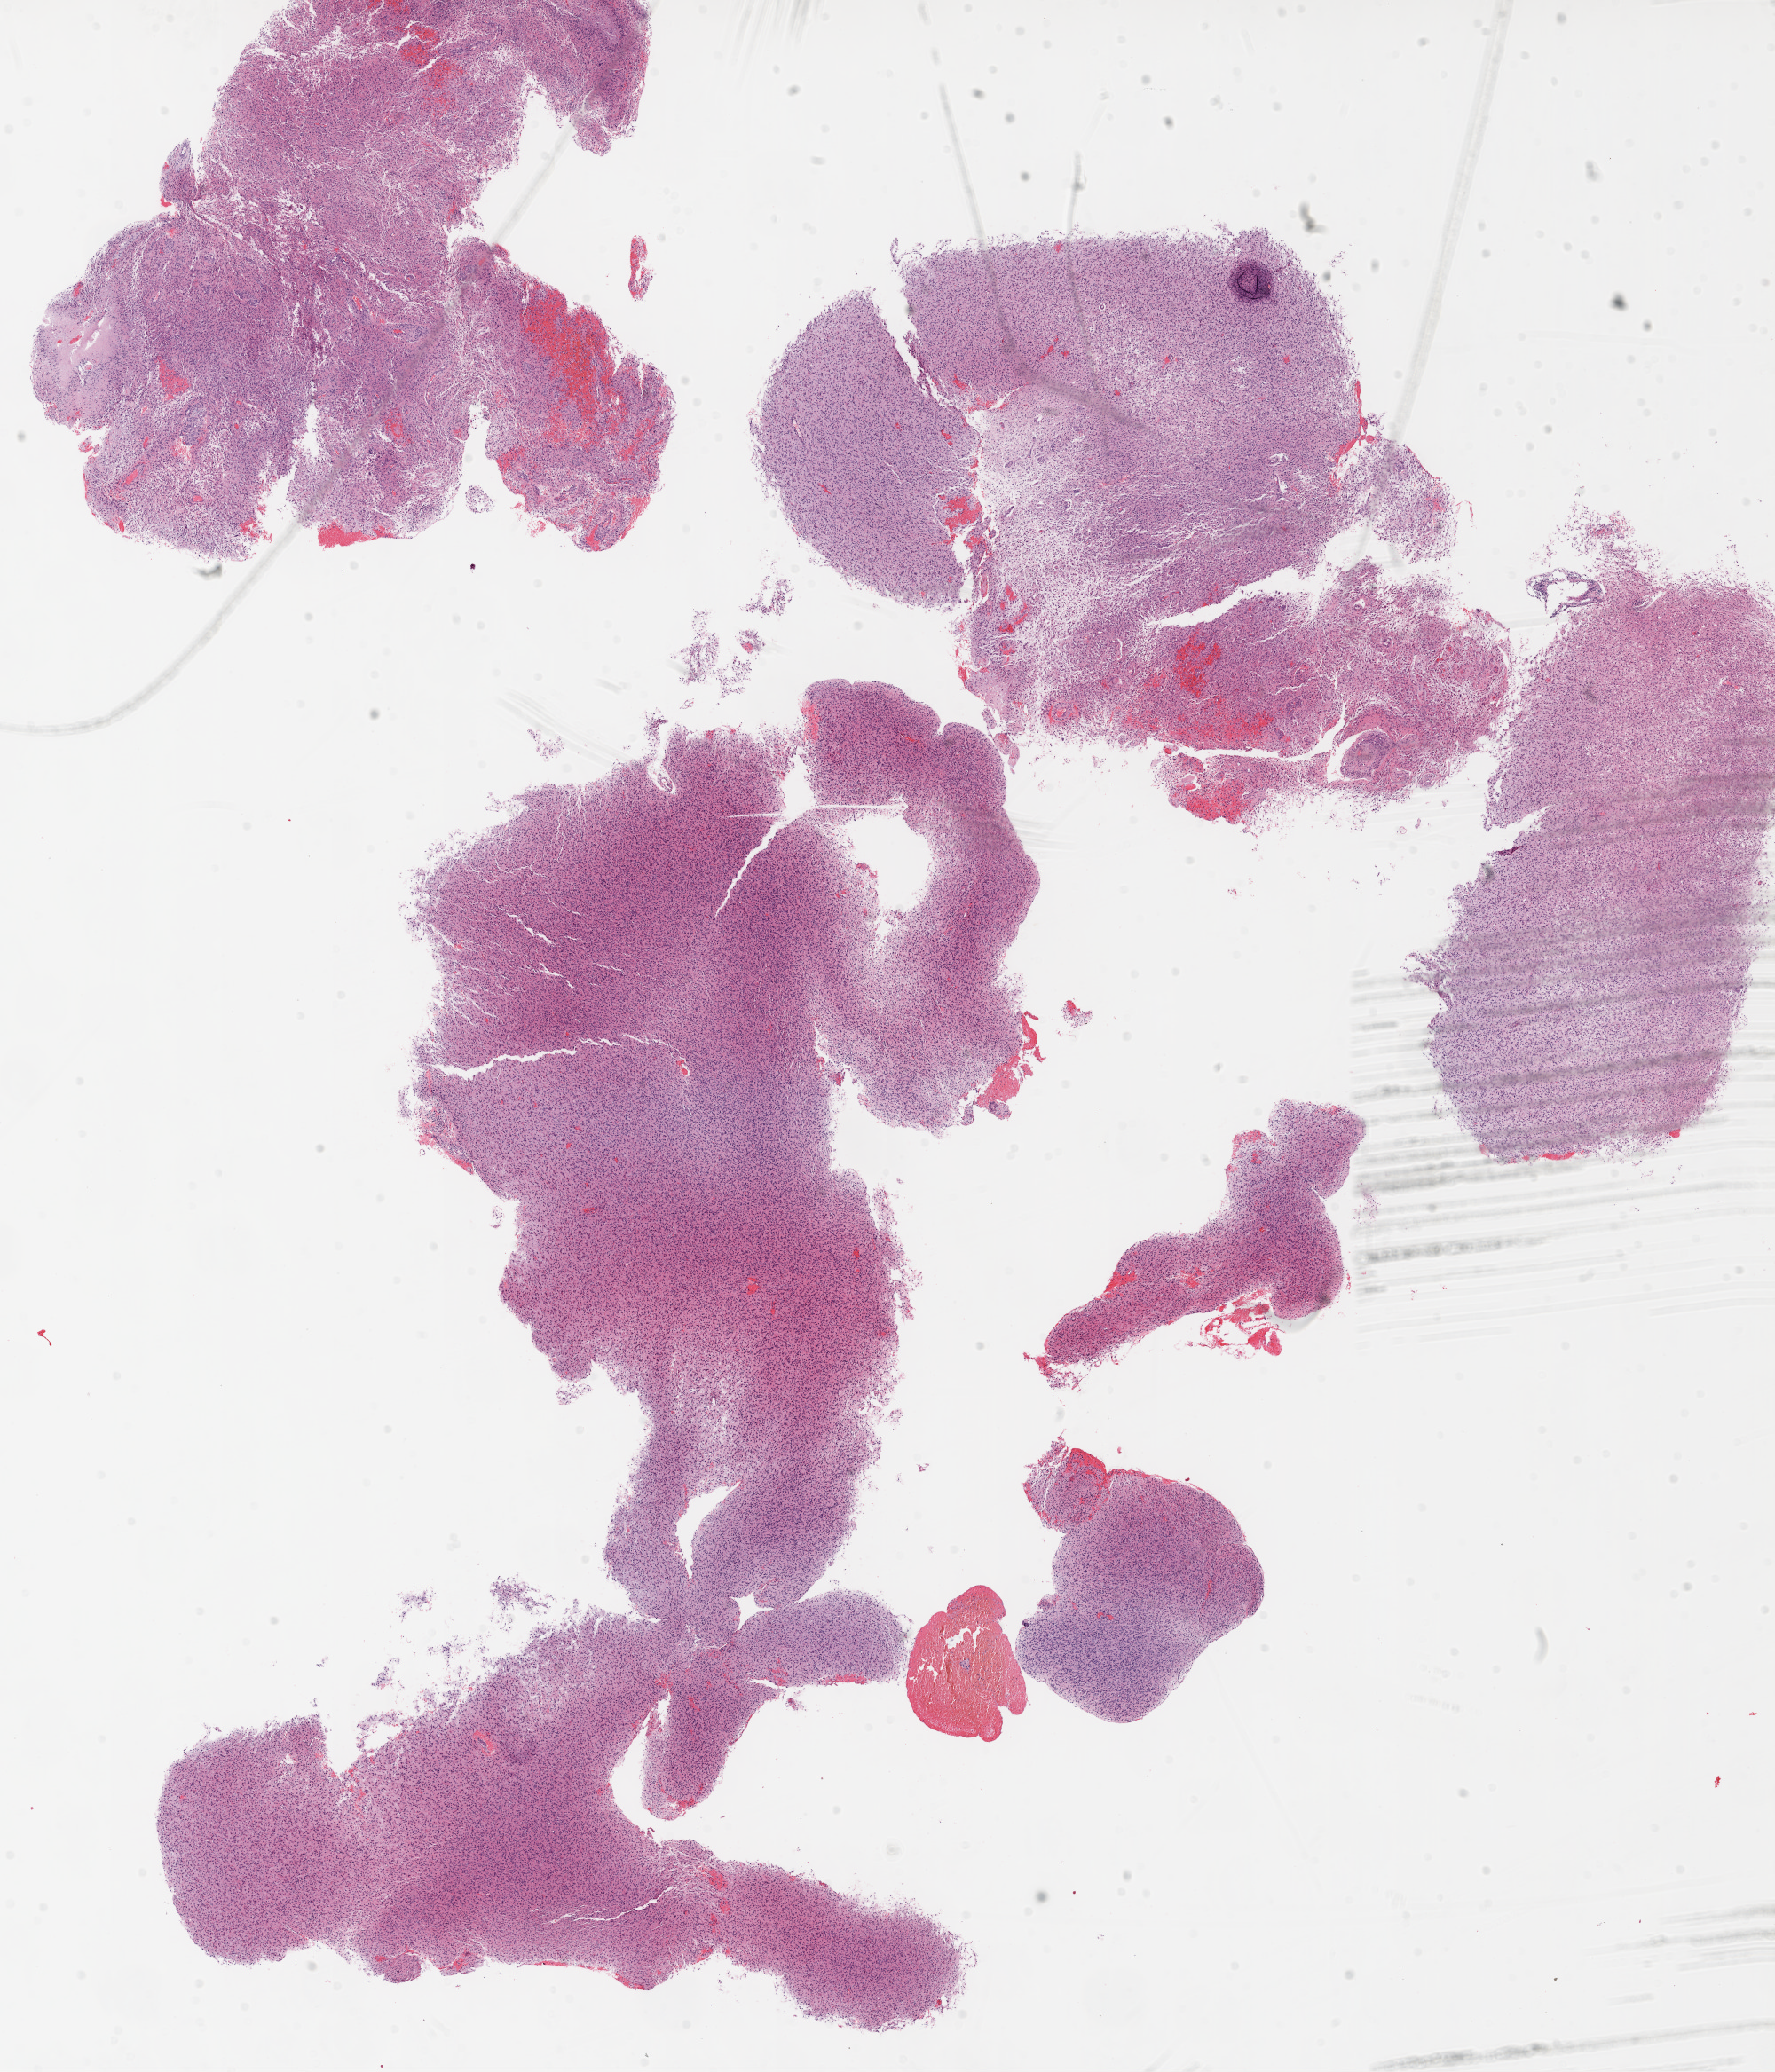
Digitized H&E-stained tissue section (whole slide), a low-resolution overview of the entire scanned area, about 16.0 x 18.7 mm (acquisition: 20x scan); formalin-fixed paraffin-embedded (FFPE) diagnostic section; primary tumour sample from the brain. Female patient; age at initial diagnosis 58 years.
Diagnosis: Glioblastoma.